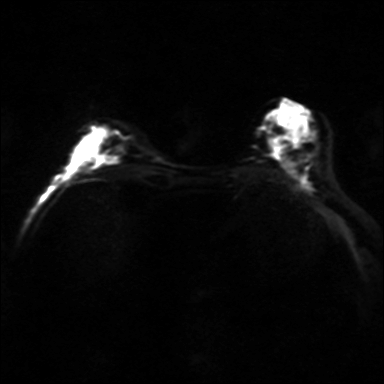
Breast MRI, one axial slice. Position 16 of 36 along the scan axis. Diffusion-weighted series; image 2 of 4 stored at this slice position (different b-values; order by instance number). 3 T. 4 mm slice thickness. 384 × 384 image matrix. Female patient.
Annotated regions visible in this slice (manually delineated by an expert):
- tumour on diffusion-weighted imaging: bounding box [x1, y1, x2, y2] px = [100, 155, 120, 166]